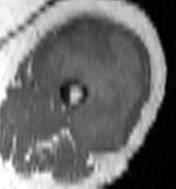
MRI of an extremity soft-tissue mass, one axial slice; position 64 of 100 along the scan axis; MR volume resampled by the dataset authors to the PET/CT grid (not the native acquisition matrix); 3.27 mm slice thickness; 176 × 189 image matrix, field of view 172 × 185 mm. Female patient. Case-level facts recorded for this patient, not image findings: histological type: undifferentiated – high grade; grade: high; site of the primary tumour: left thigh.
Outlined on this slice (expert contour drawn on MRI and transferred to this co-registered scan by the dataset authors):
- gross tumour volume including surrounding oedema: bounding box [x1, y1, x2, y2] px = [46, 23, 143, 154]
- gross tumour volume (mass): [46, 23, 143, 154]